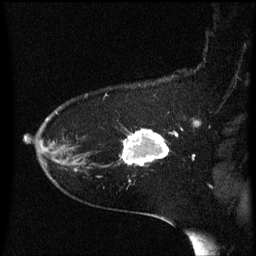
Breast MRI (dynamic contrast-enhanced), one sagittal slice; position 44 of 60 along the scan axis; dynamic contrast-enhanced series, image 2 of 3 at this slice position (ordered by acquisition); 1.5 T; TE 4.2 ms, TR 8.4 ms; 2 mm slice thickness; 256 × 256 image matrix, field of view 200 × 200 mm. Female patient, age 54 years. Case-level facts recorded for this patient, not image findings: setting: breast cancer imaged before/during neoadjuvant chemotherapy; receptor status: HR-positive, HER2-negative.
Annotated regions visible in this slice (semi-automatic segmentation, software-assisted and operator-edited):
- analysis volume of interest (the breast-tissue region the enhancement analysis was run in; not a lesion): bounding box (x1, y1, x2, y2) in pixels: (123, 130, 170, 167)
- tumour enhancement mask (voxels above the 70 % enhancement threshold inside the analysis volume of interest): (123, 130, 170, 167)